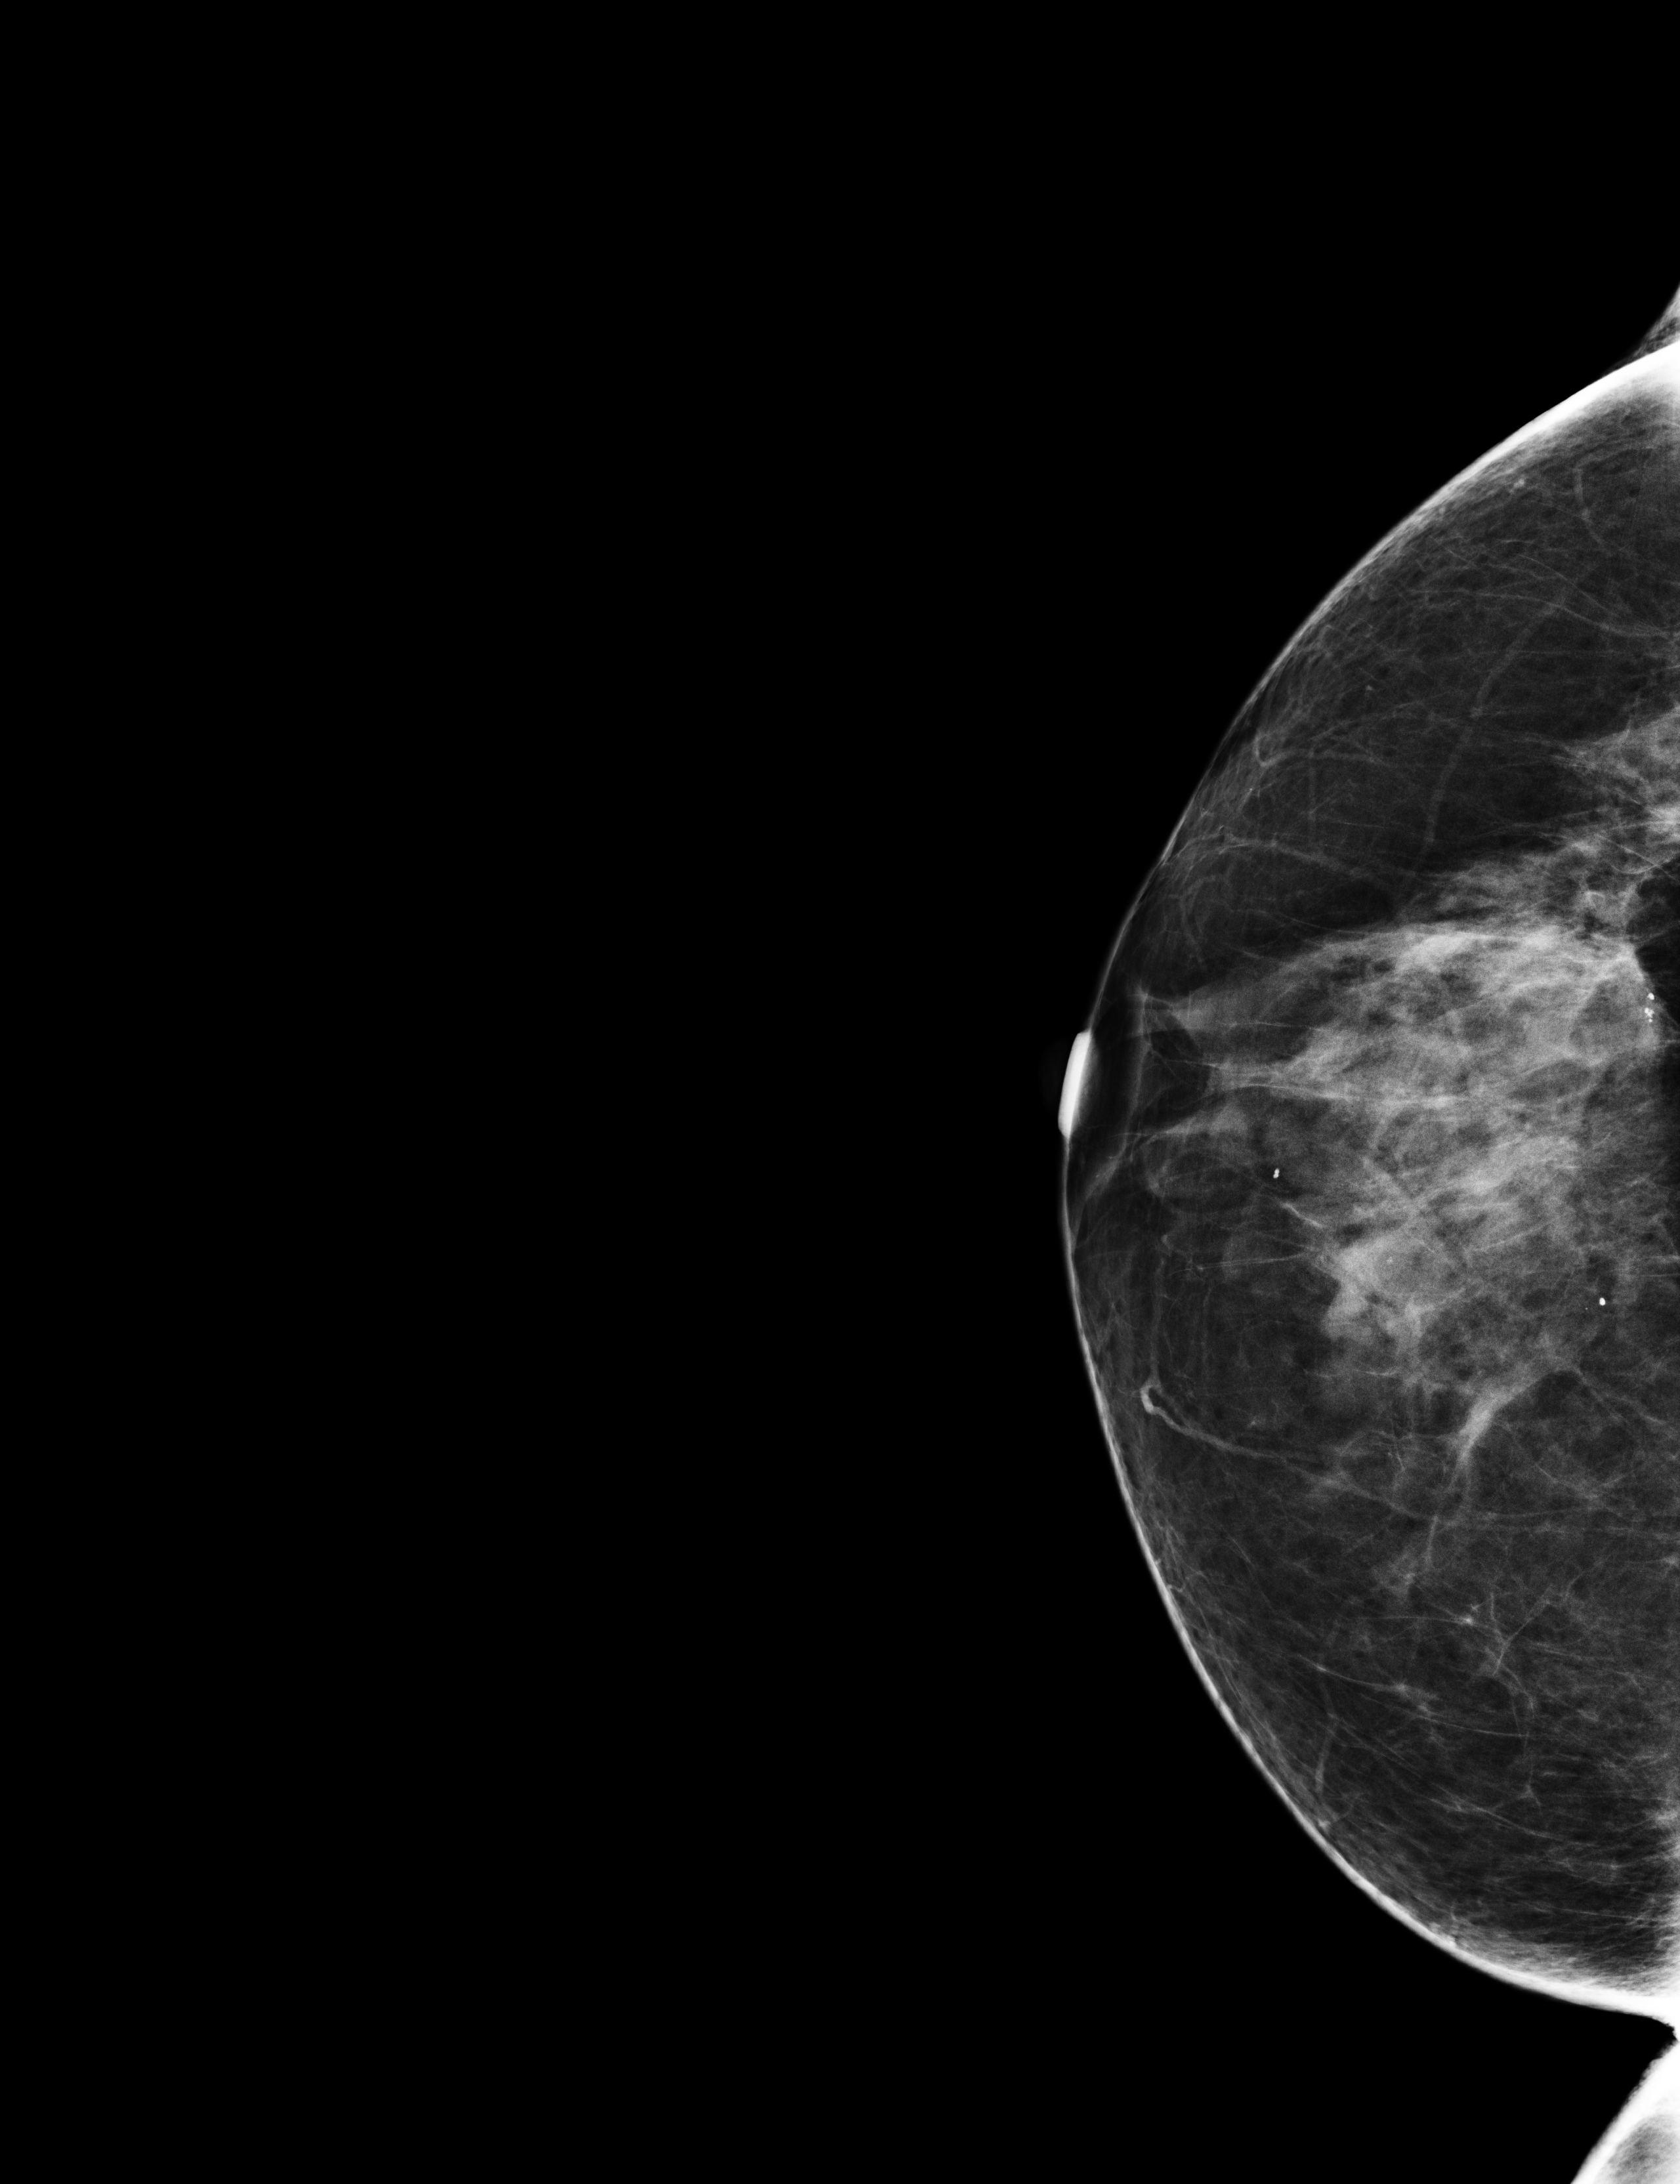
Digital mammogram (FFDM); right breast; cranio-caudal projection; annual screening mammography examination; compressed breast thickness 60 mm. Female patient, age 67 years.
BI-RADS breast density category at the screening exam (both breasts, scale 1–4): 3. Final BI-RADS category for the screening round (tomosynthesis exam, both breasts): category 1. Recall: no recall after this screen.